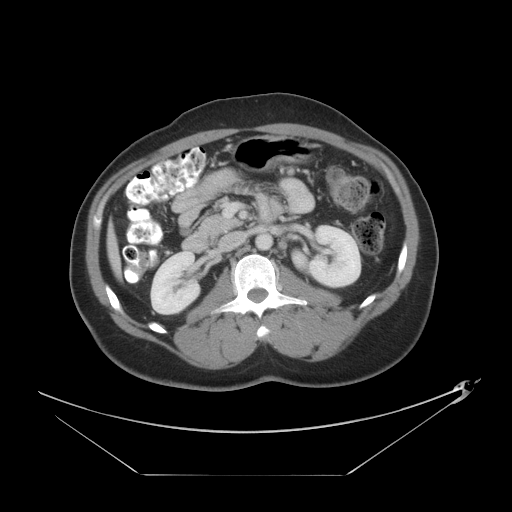
Contrast-enhanced abdominal CT, one axial slice; slice 16 of 44 in the series (ordered by position); 120 kVp; soft-tissue window (W 400 / L 40 HU); 5 mm slice thickness; 512 × 512 image matrix, field of view 466 × 466 mm. Male patient, age 49 years. Case-level facts recorded for this patient, not image findings: diagnosis: colorectal cancer liver metastases, imaged before liver resection; multiple liver metastases: no; largest metastasis: 8.5 cm; disease in both lobes: yes.
Outlined on this slice (manually delineated by an expert):
- liver: bounding box <107,226,121,276> (left, top, right, bottom; pixels)